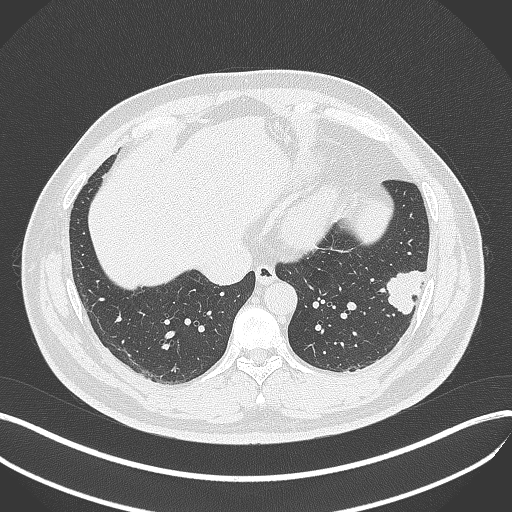
Chest CT, one axial slice. Position 127 of 429 along the scan axis. Reconstruction kernel B70f. Lung window (W 1500 / L -600 HU). 1 mm slice thickness. 512 × 512 image matrix, field of view 400 × 400 mm. Patient: male, 39 years. Case-level facts recorded for this patient, not image findings: clinical TNM (as recorded): T2a N0 M0; histopathological grade: G2-3.
Annotated regions visible in this slice (bounding box drawn by a radiologist):
- lung tumour (recorded histology: adenocarcinoma): bounding box <381,267,428,321> (left, top, right, bottom; pixels)